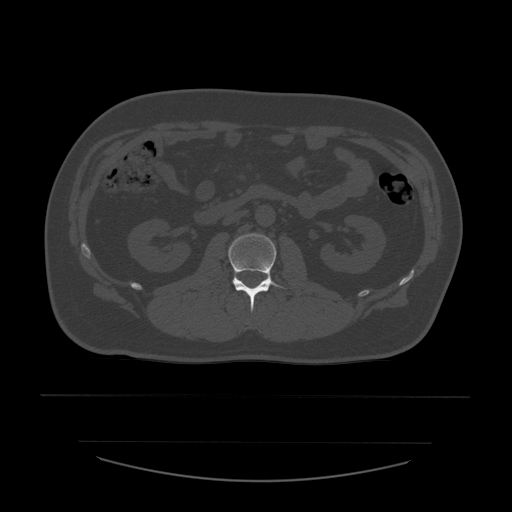
CT including the spine, one axial slice; slice 199 of 532 in the series (ordered by position); 120 kVp; bone window (W 1800 / L 400 HU); 1.25 mm slice thickness; 512 × 512 image matrix. Patient age 44 years. From the clinical record (not read from this slice): primary cancer: soft tissue sarcoma.
Outlined on this slice (semi-automatic segmentation, software-assisted and operator-edited):
- L2 vertebra: bounding box [x1, y1, x2, y2] px = [229, 234, 286, 311]